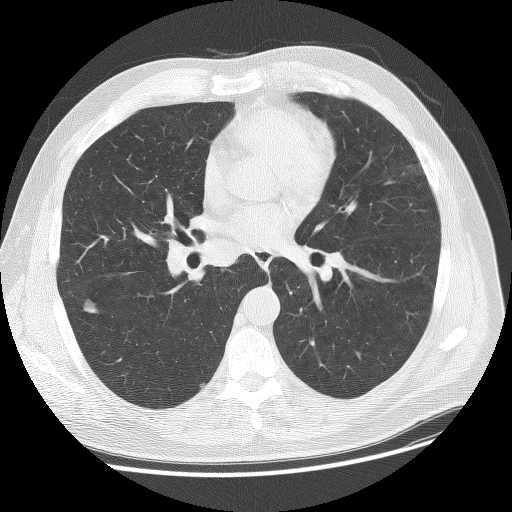
Low-dose screening chest CT, one axial slice; slice 75 of 137 in the series (ordered by position); reconstruction kernel BONE; lung window (W 1500 / L -600 HU); 2.5 mm slice thickness; 512 × 512 image matrix, field of view 380 × 380 mm.
Annotated regions visible in this slice (expert manual segmentation):
- lesion 2 (tumor, lower lobe of right lung): bounding box <85,302,97,313> (left, top, right, bottom; pixels)